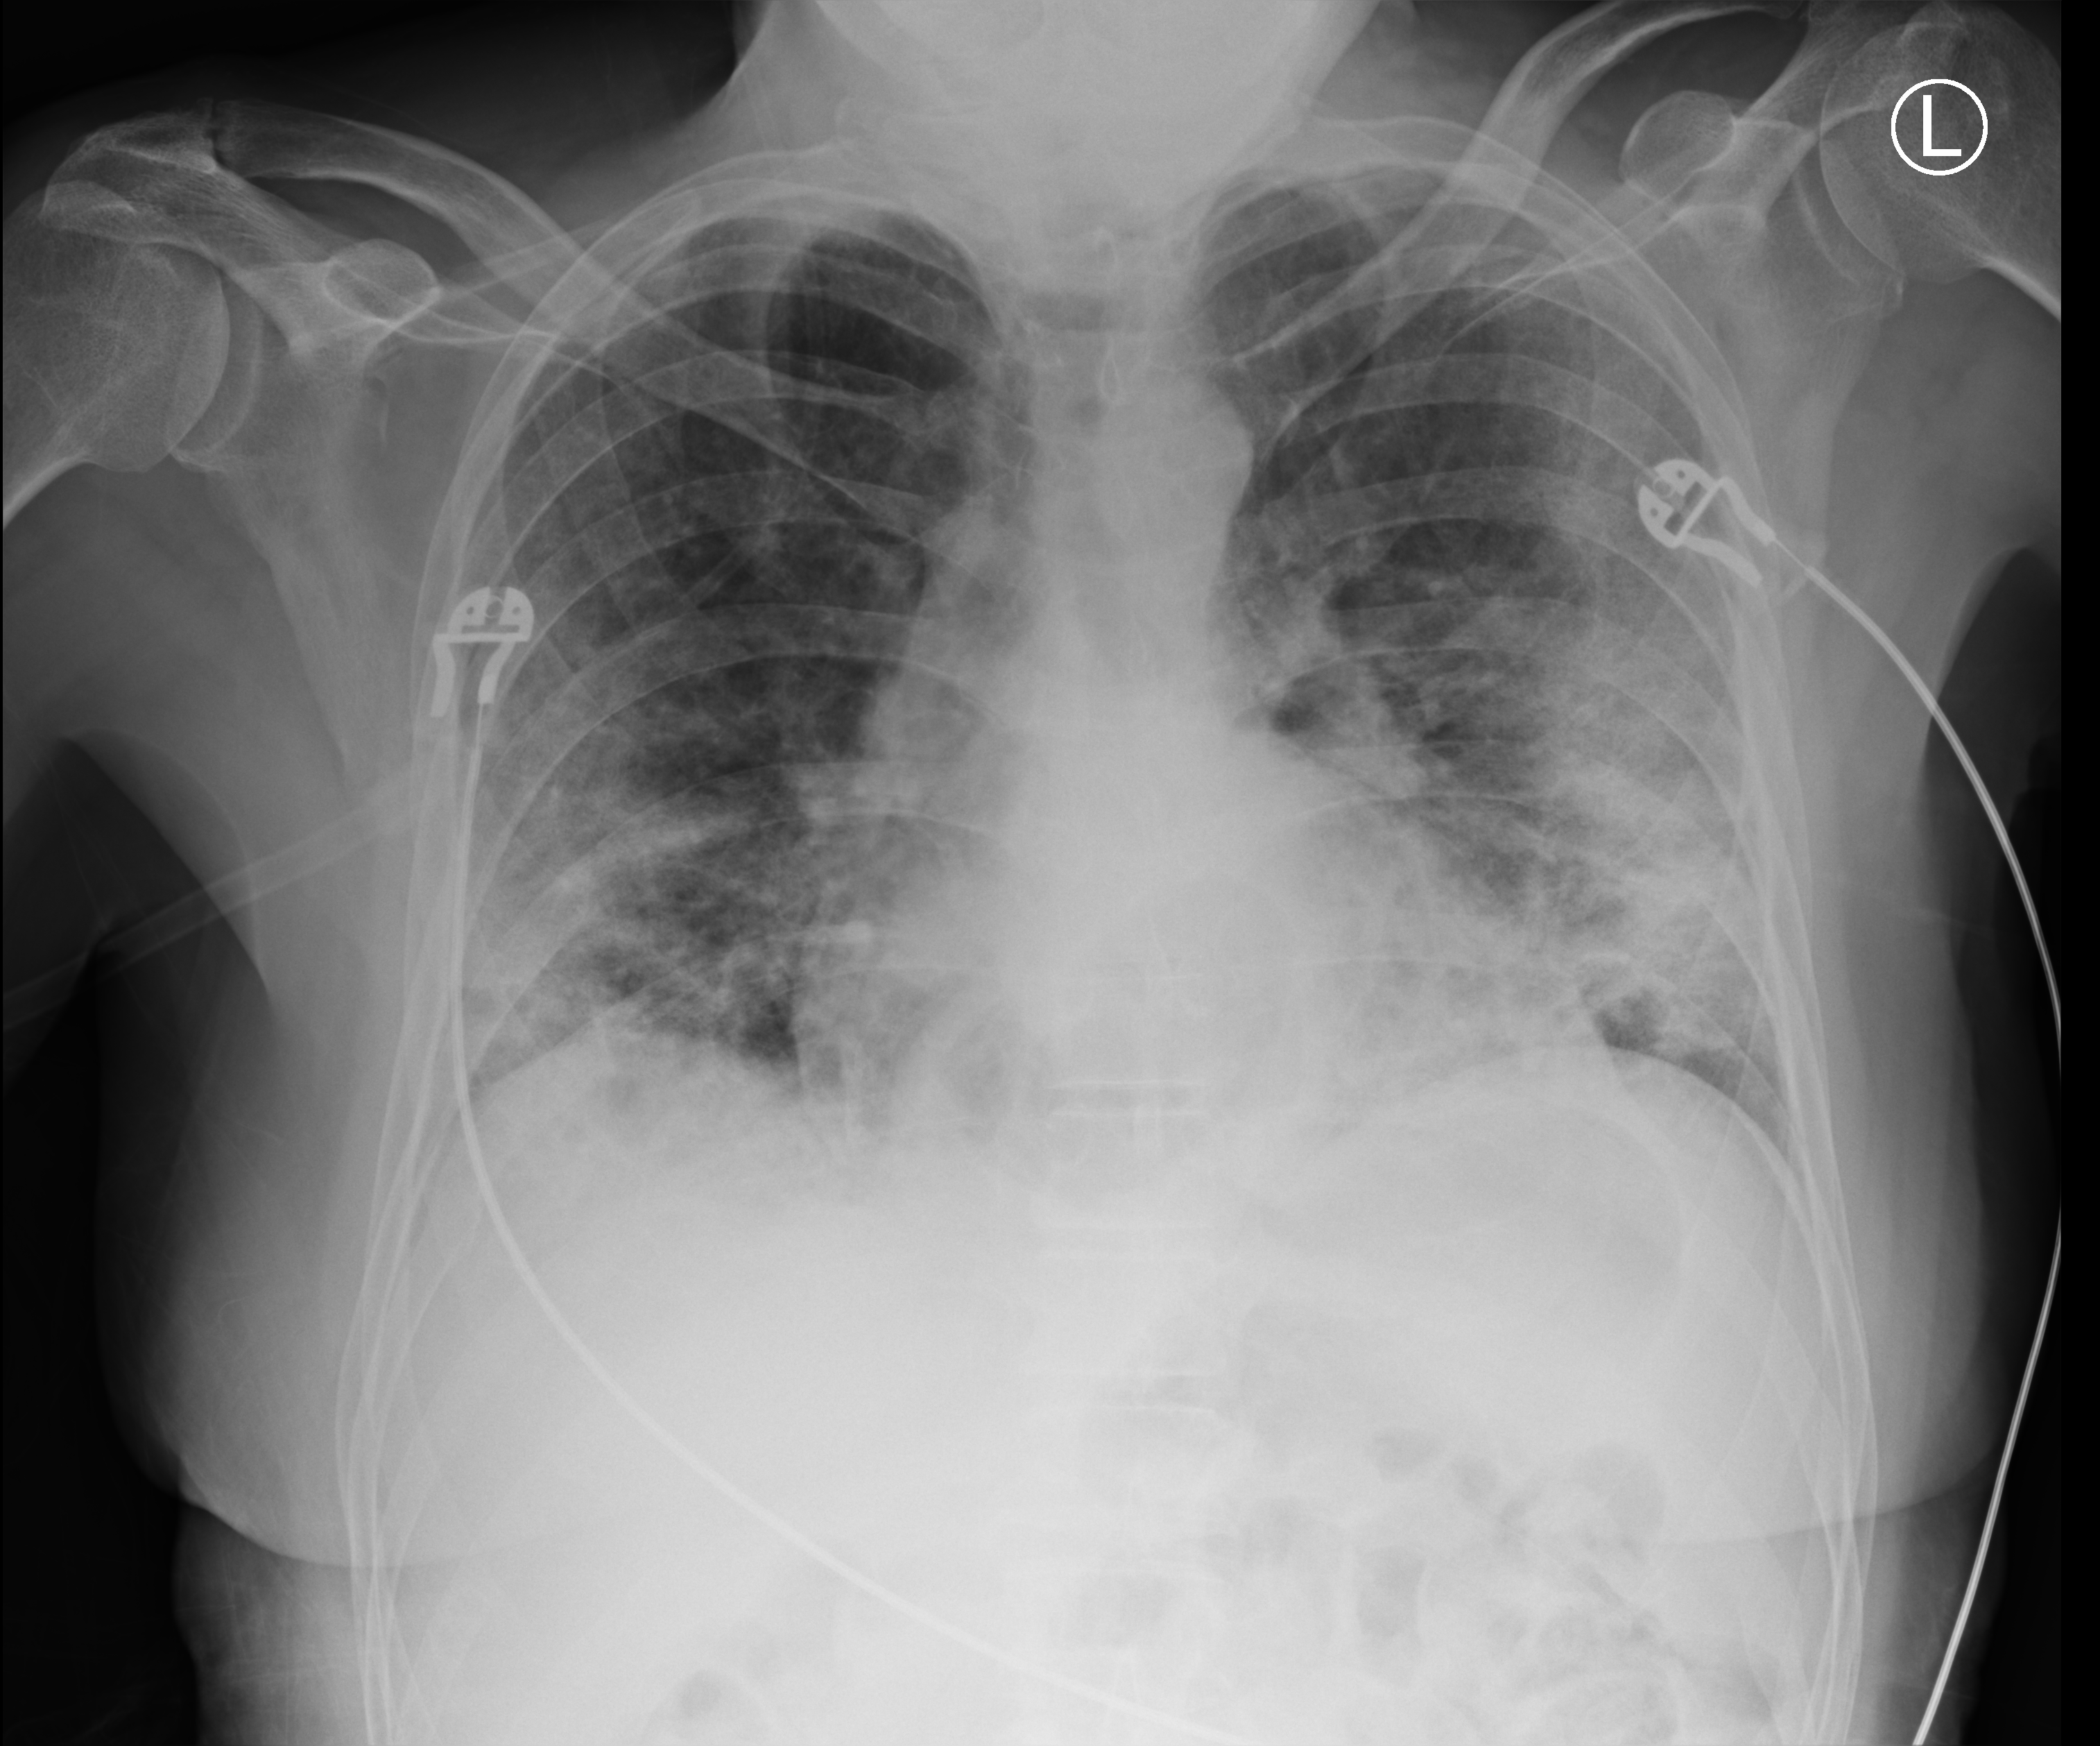
Bedside chest radiograph (computed radiography), anteroposterior (AP) projection. Male patient hospitalised with COVID-19, age 60–74 years.
From the hospital-stay record, not from the radiograph (when in the stay this image was taken is not recorded): admitted to intensive care during this hospital stay: no.